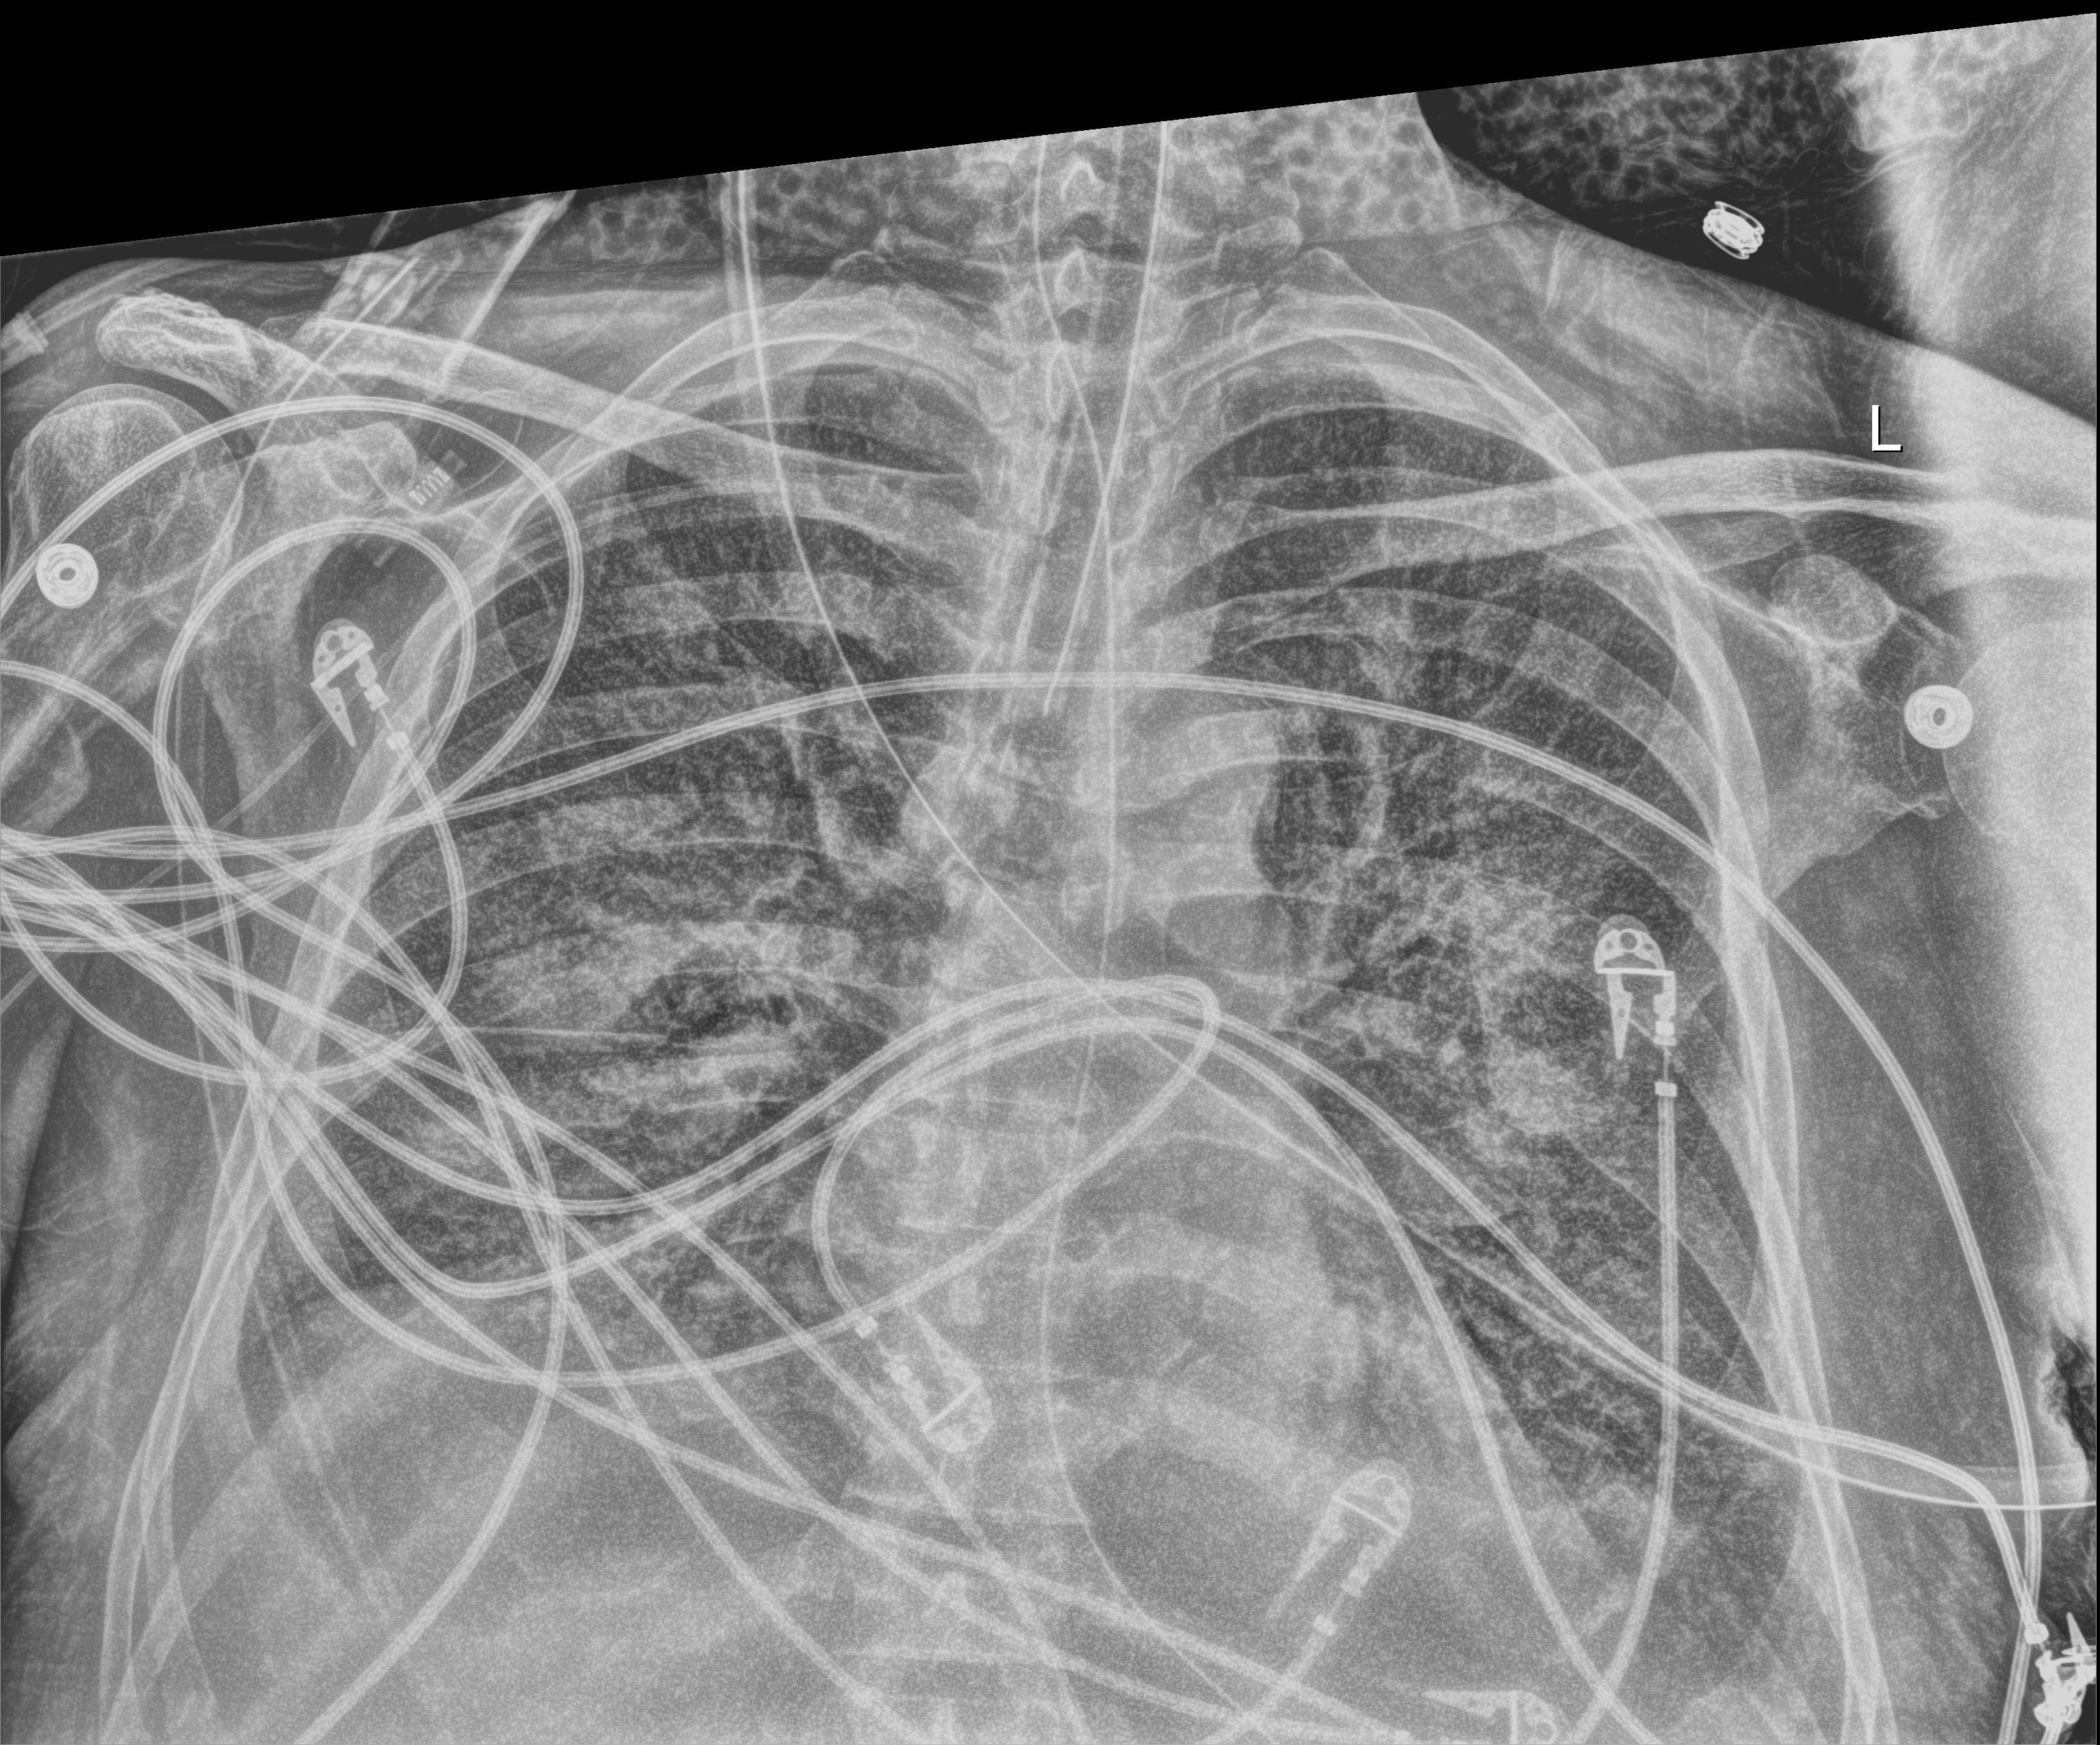
Portable chest radiograph, anteroposterior (AP) projection. Male patient hospitalised with COVID-19, age 60–74 years.
Admission-level facts for this patient (not findings on this image; timing relative to this image not recorded): admitted to intensive care during this hospital stay: yes.